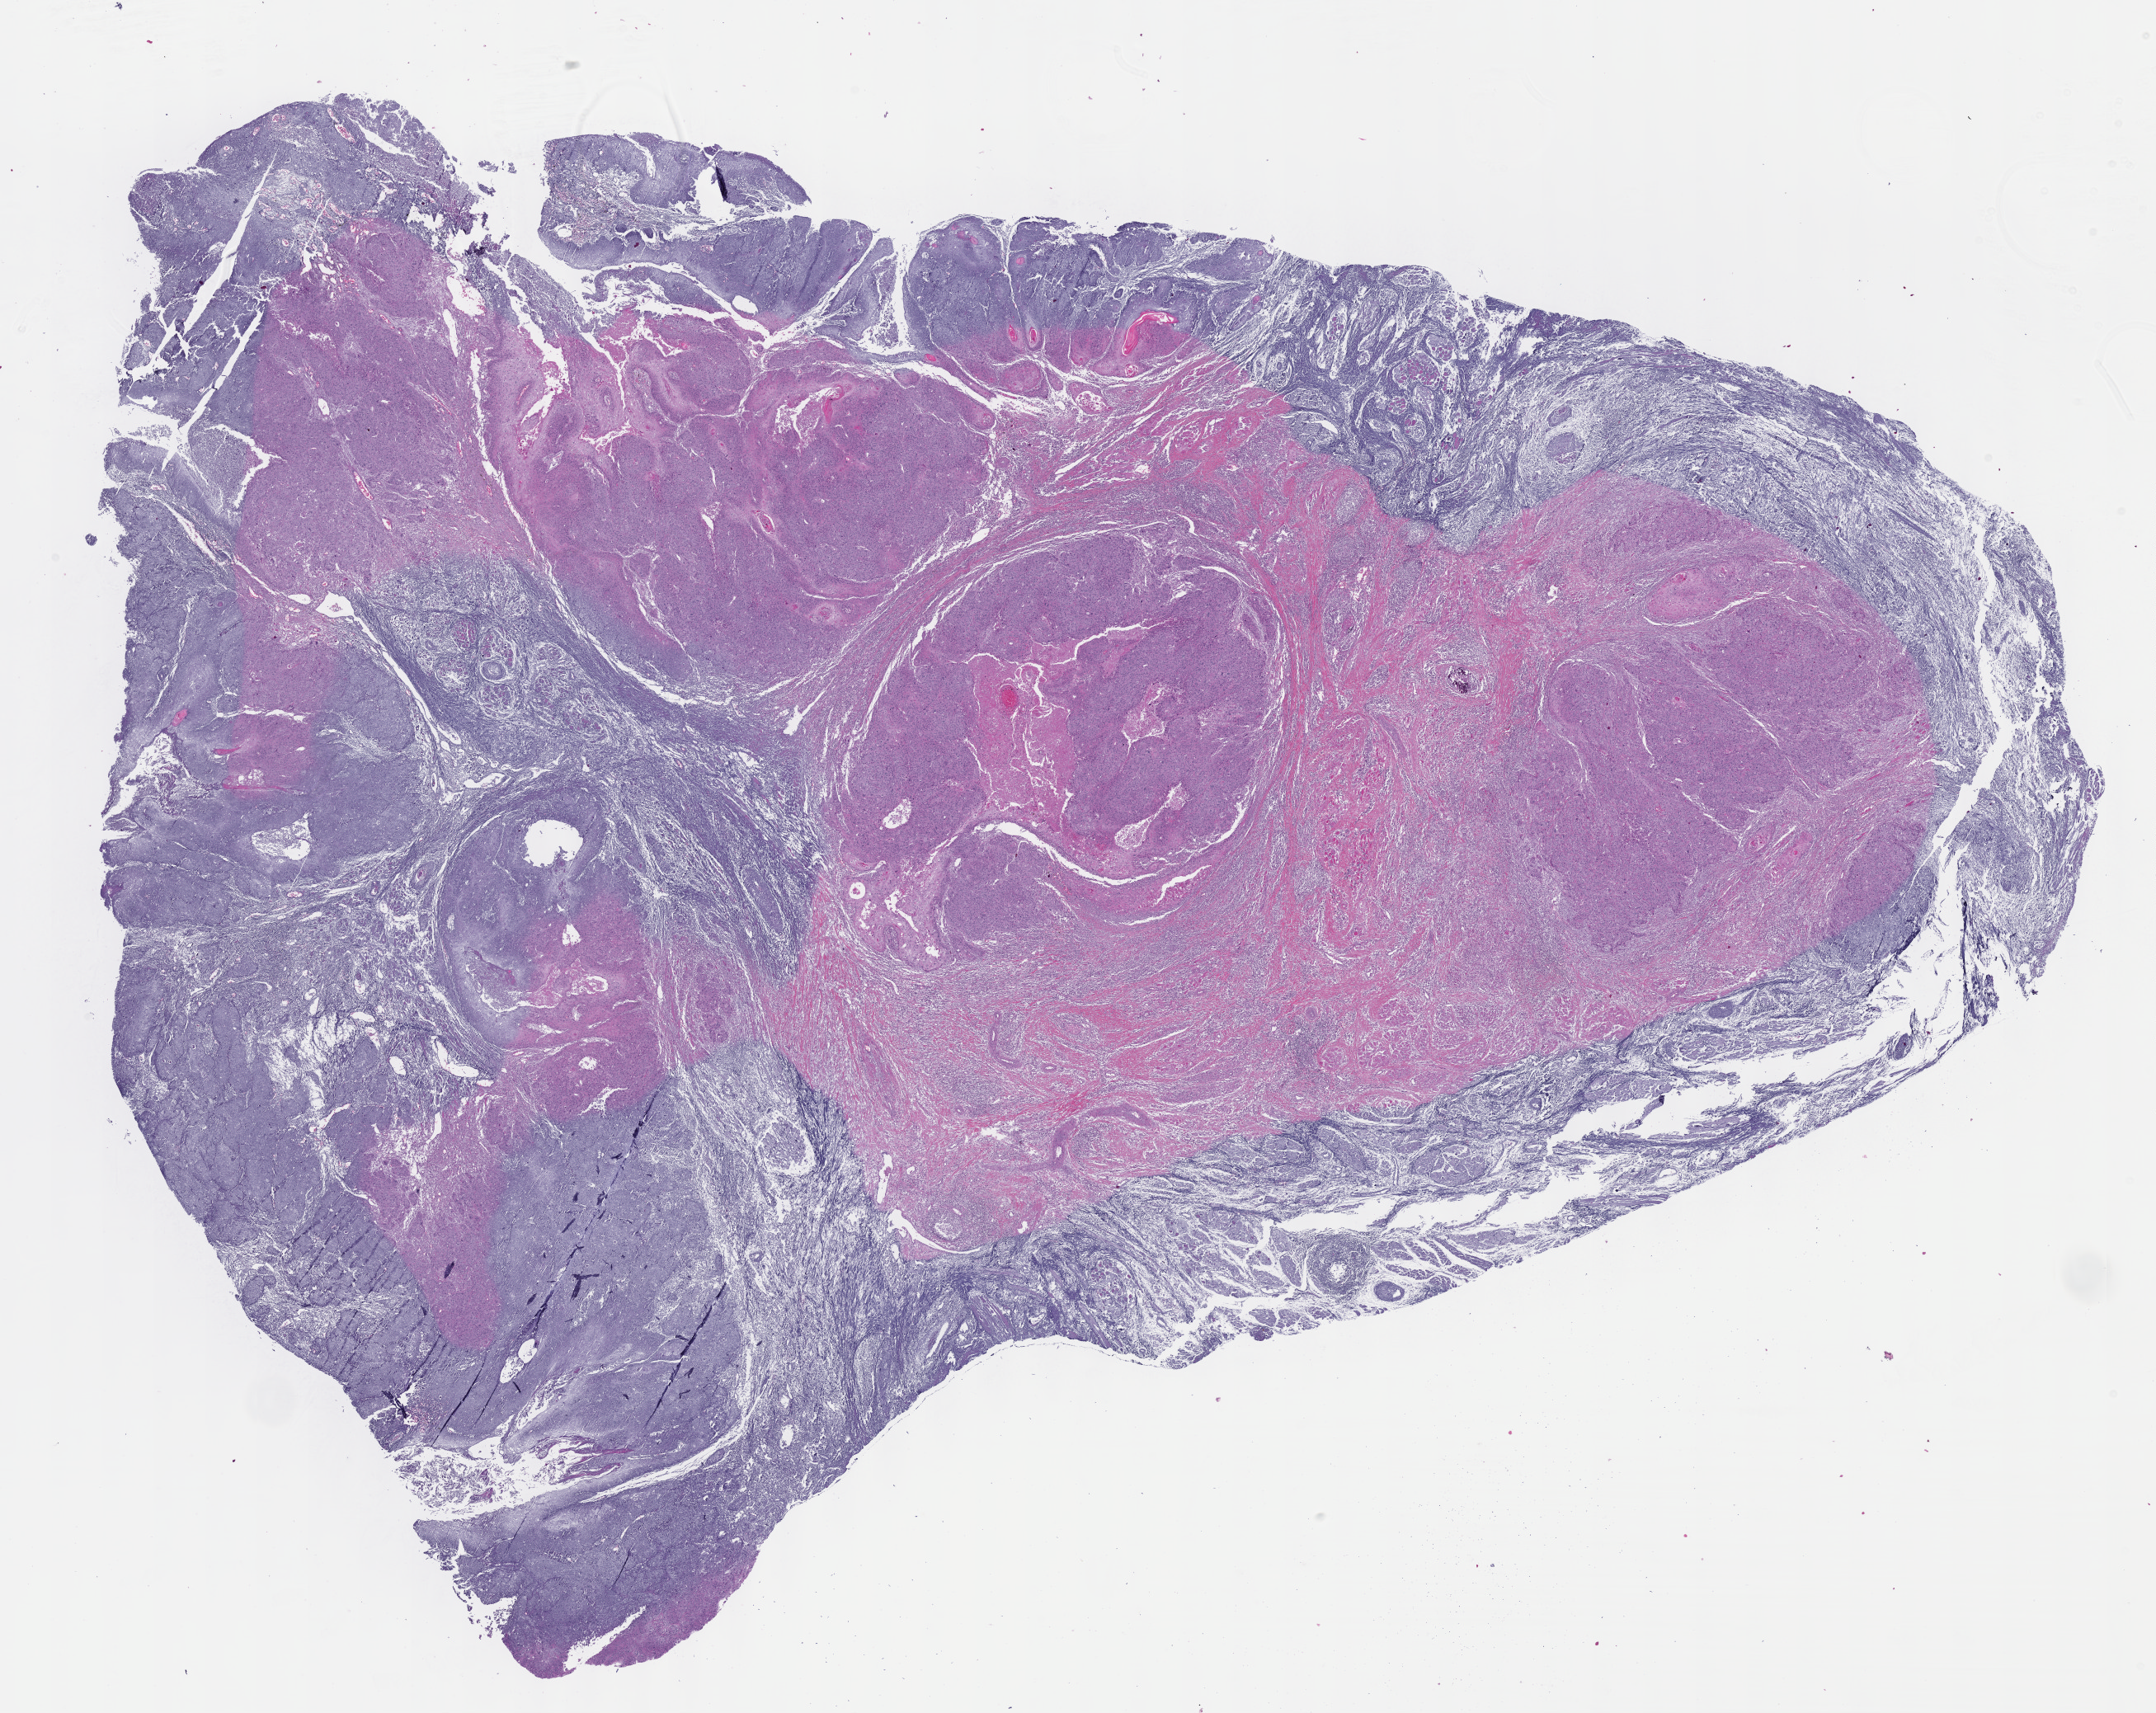
Whole-slide histology image, H&E, a low-resolution overview of the entire scanned area, about 21.1 x 16.8 mm. FFPE section. Head and neck, primary tumour sample. Male, age 48 years at initial diagnosis. Histologic grade: G2 (moderately differentiated).
Pathologic diagnosis: Squamous cell carcinoma, NOS (tongue, NOS). AJCC pathologic stage: III (7th edition).